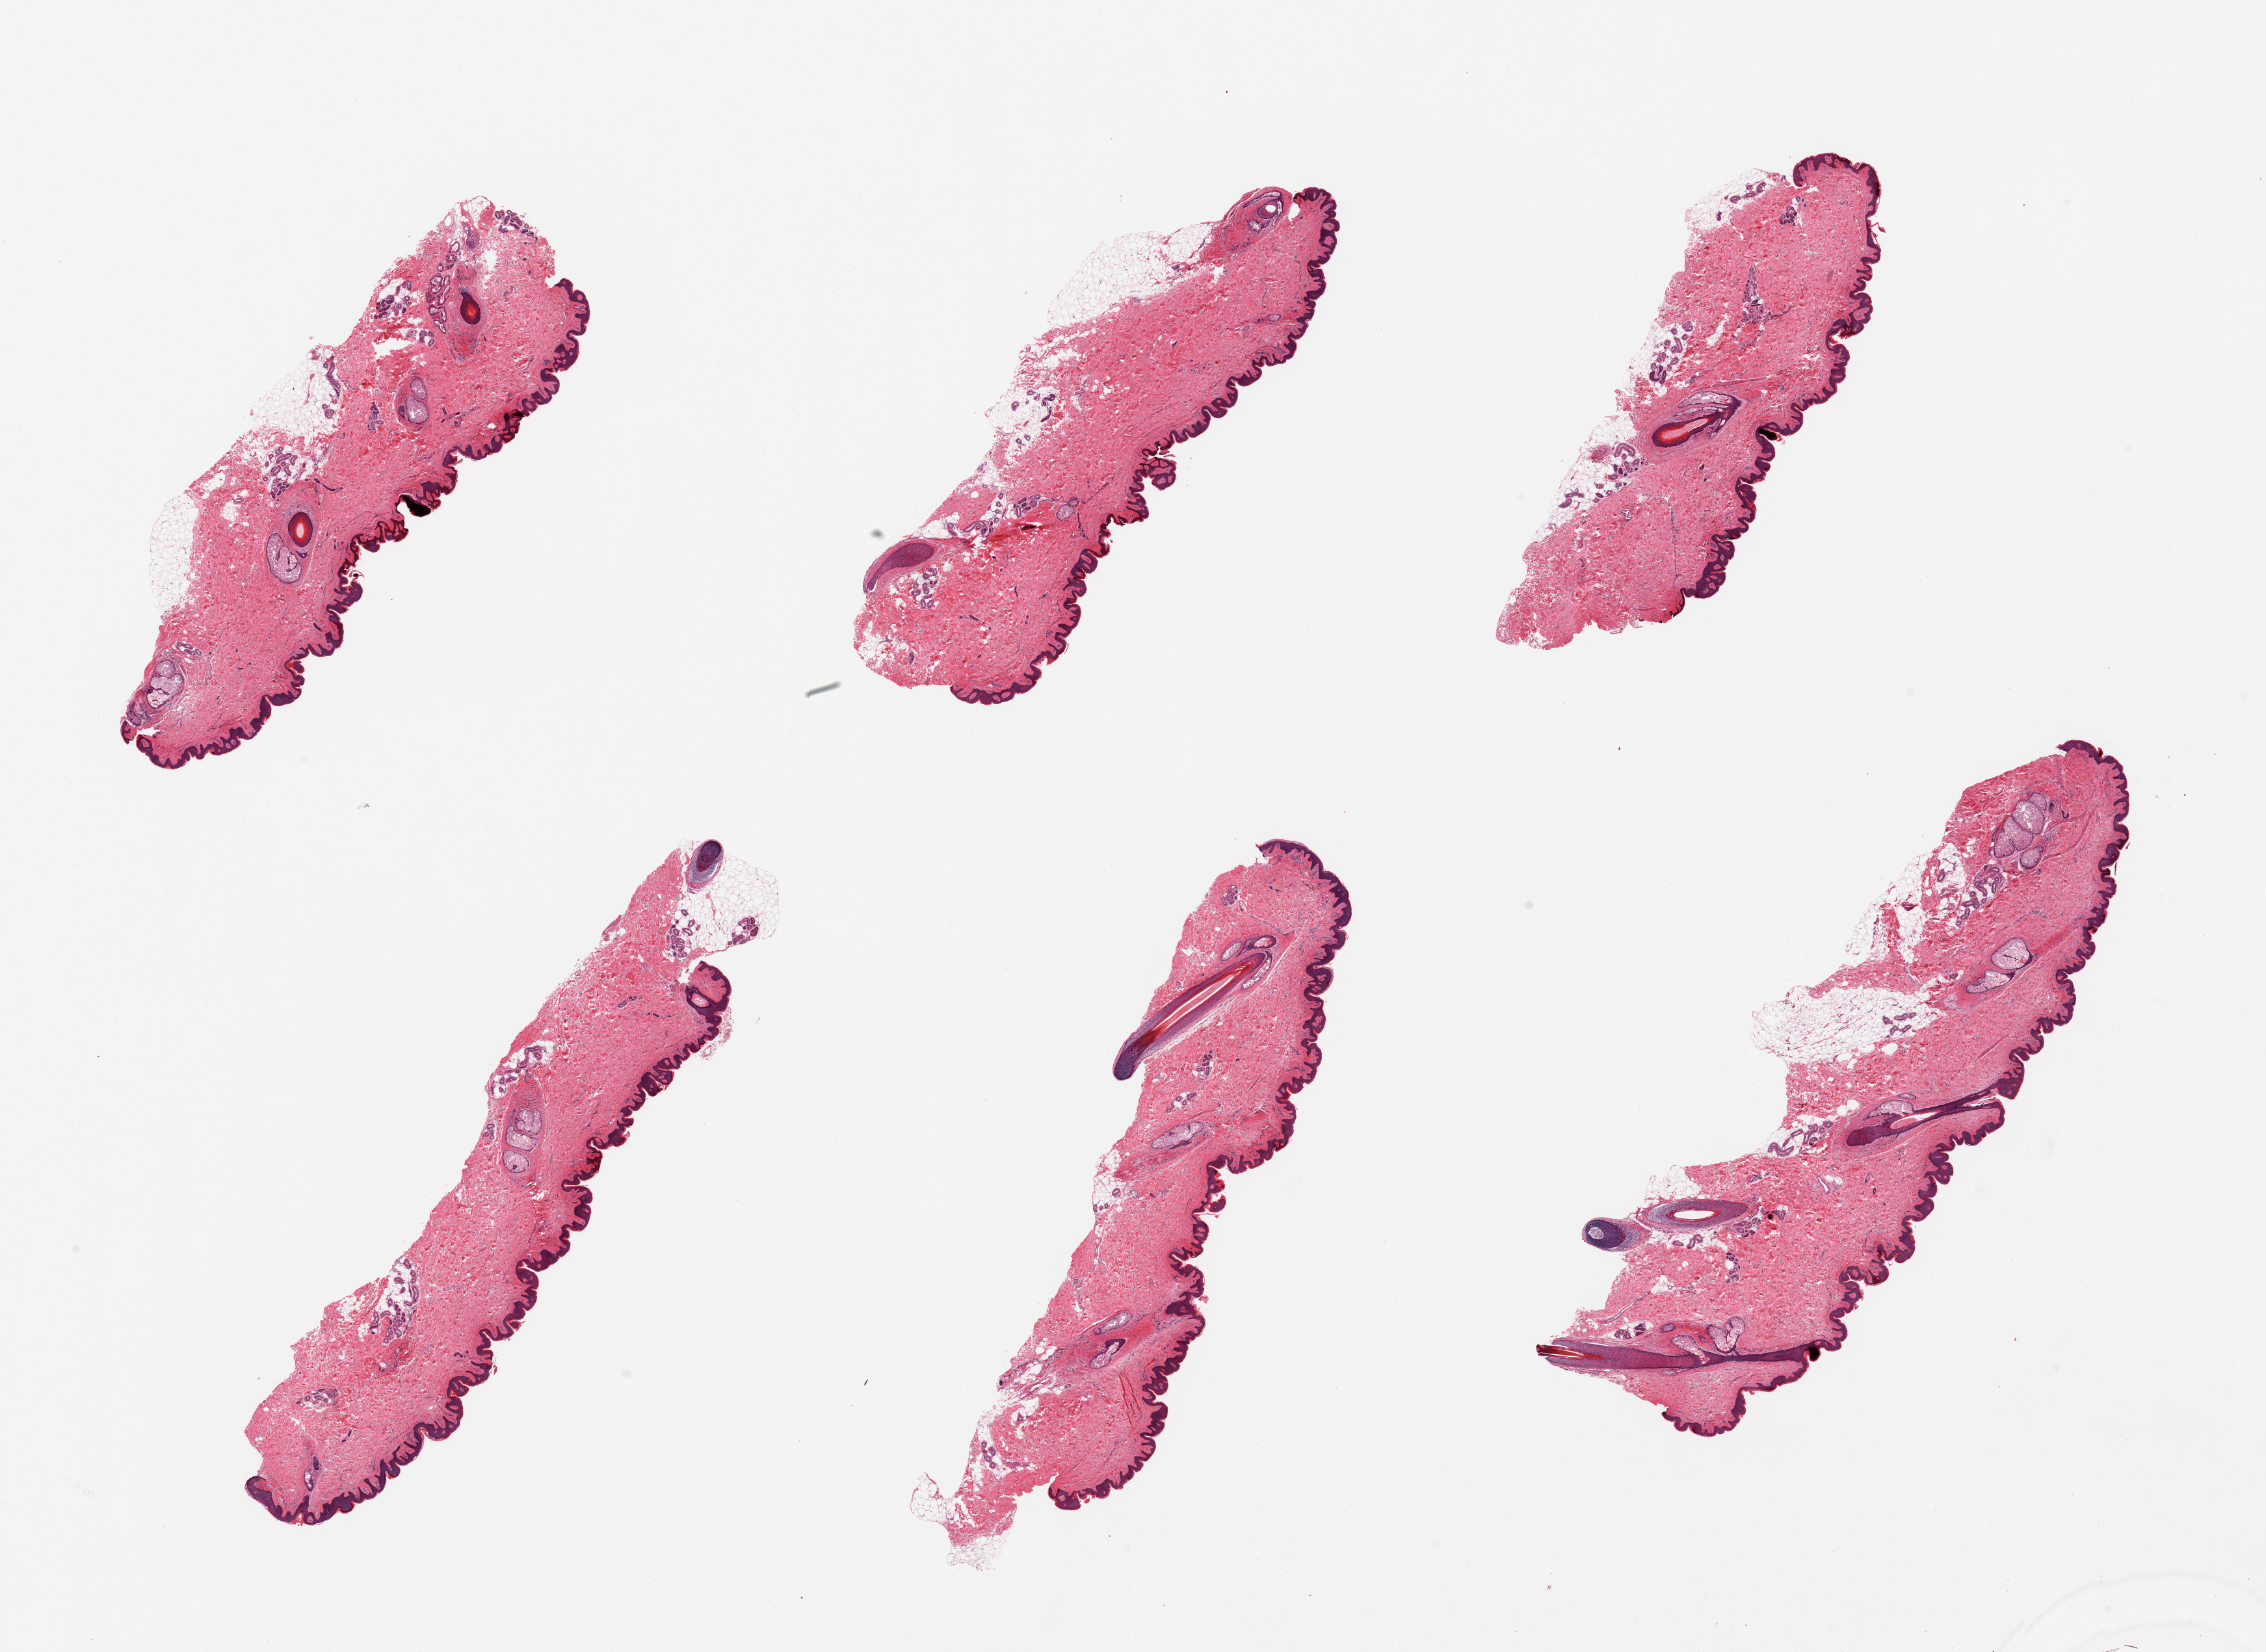
Digitized hematoxylin and eosin (H&E)-stained section — low-resolution overview of the scanned area, about 27.6 x 20.1 mm, PAXgene-fixed, paraffin-embedded tissue, target tissue: skin of suprapubic region, donor tissue sample. Donor: male.
- reviewer comment on this tissue sample: 6 pieces. miinmal adherent dermal fat; squamous epithelium is ~30-40 microns